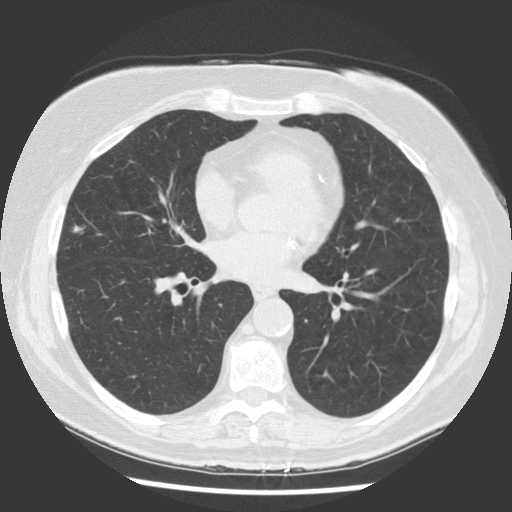
Low-dose screening chest CT, one axial slice; slice 75 of 142 in the series (ordered by position); reconstruction kernel STANDARD; lung window (W 1500 / L -600 HU); 2.5 mm slice thickness; 512 × 512 image matrix, field of view 340 × 340 mm.
Annotated regions visible in this slice (manually delineated by an expert):
- lesion 1 (tumor, middle lobe of right lung): bounding box (x1, y1, x2, y2) in pixels: (71, 223, 86, 235)